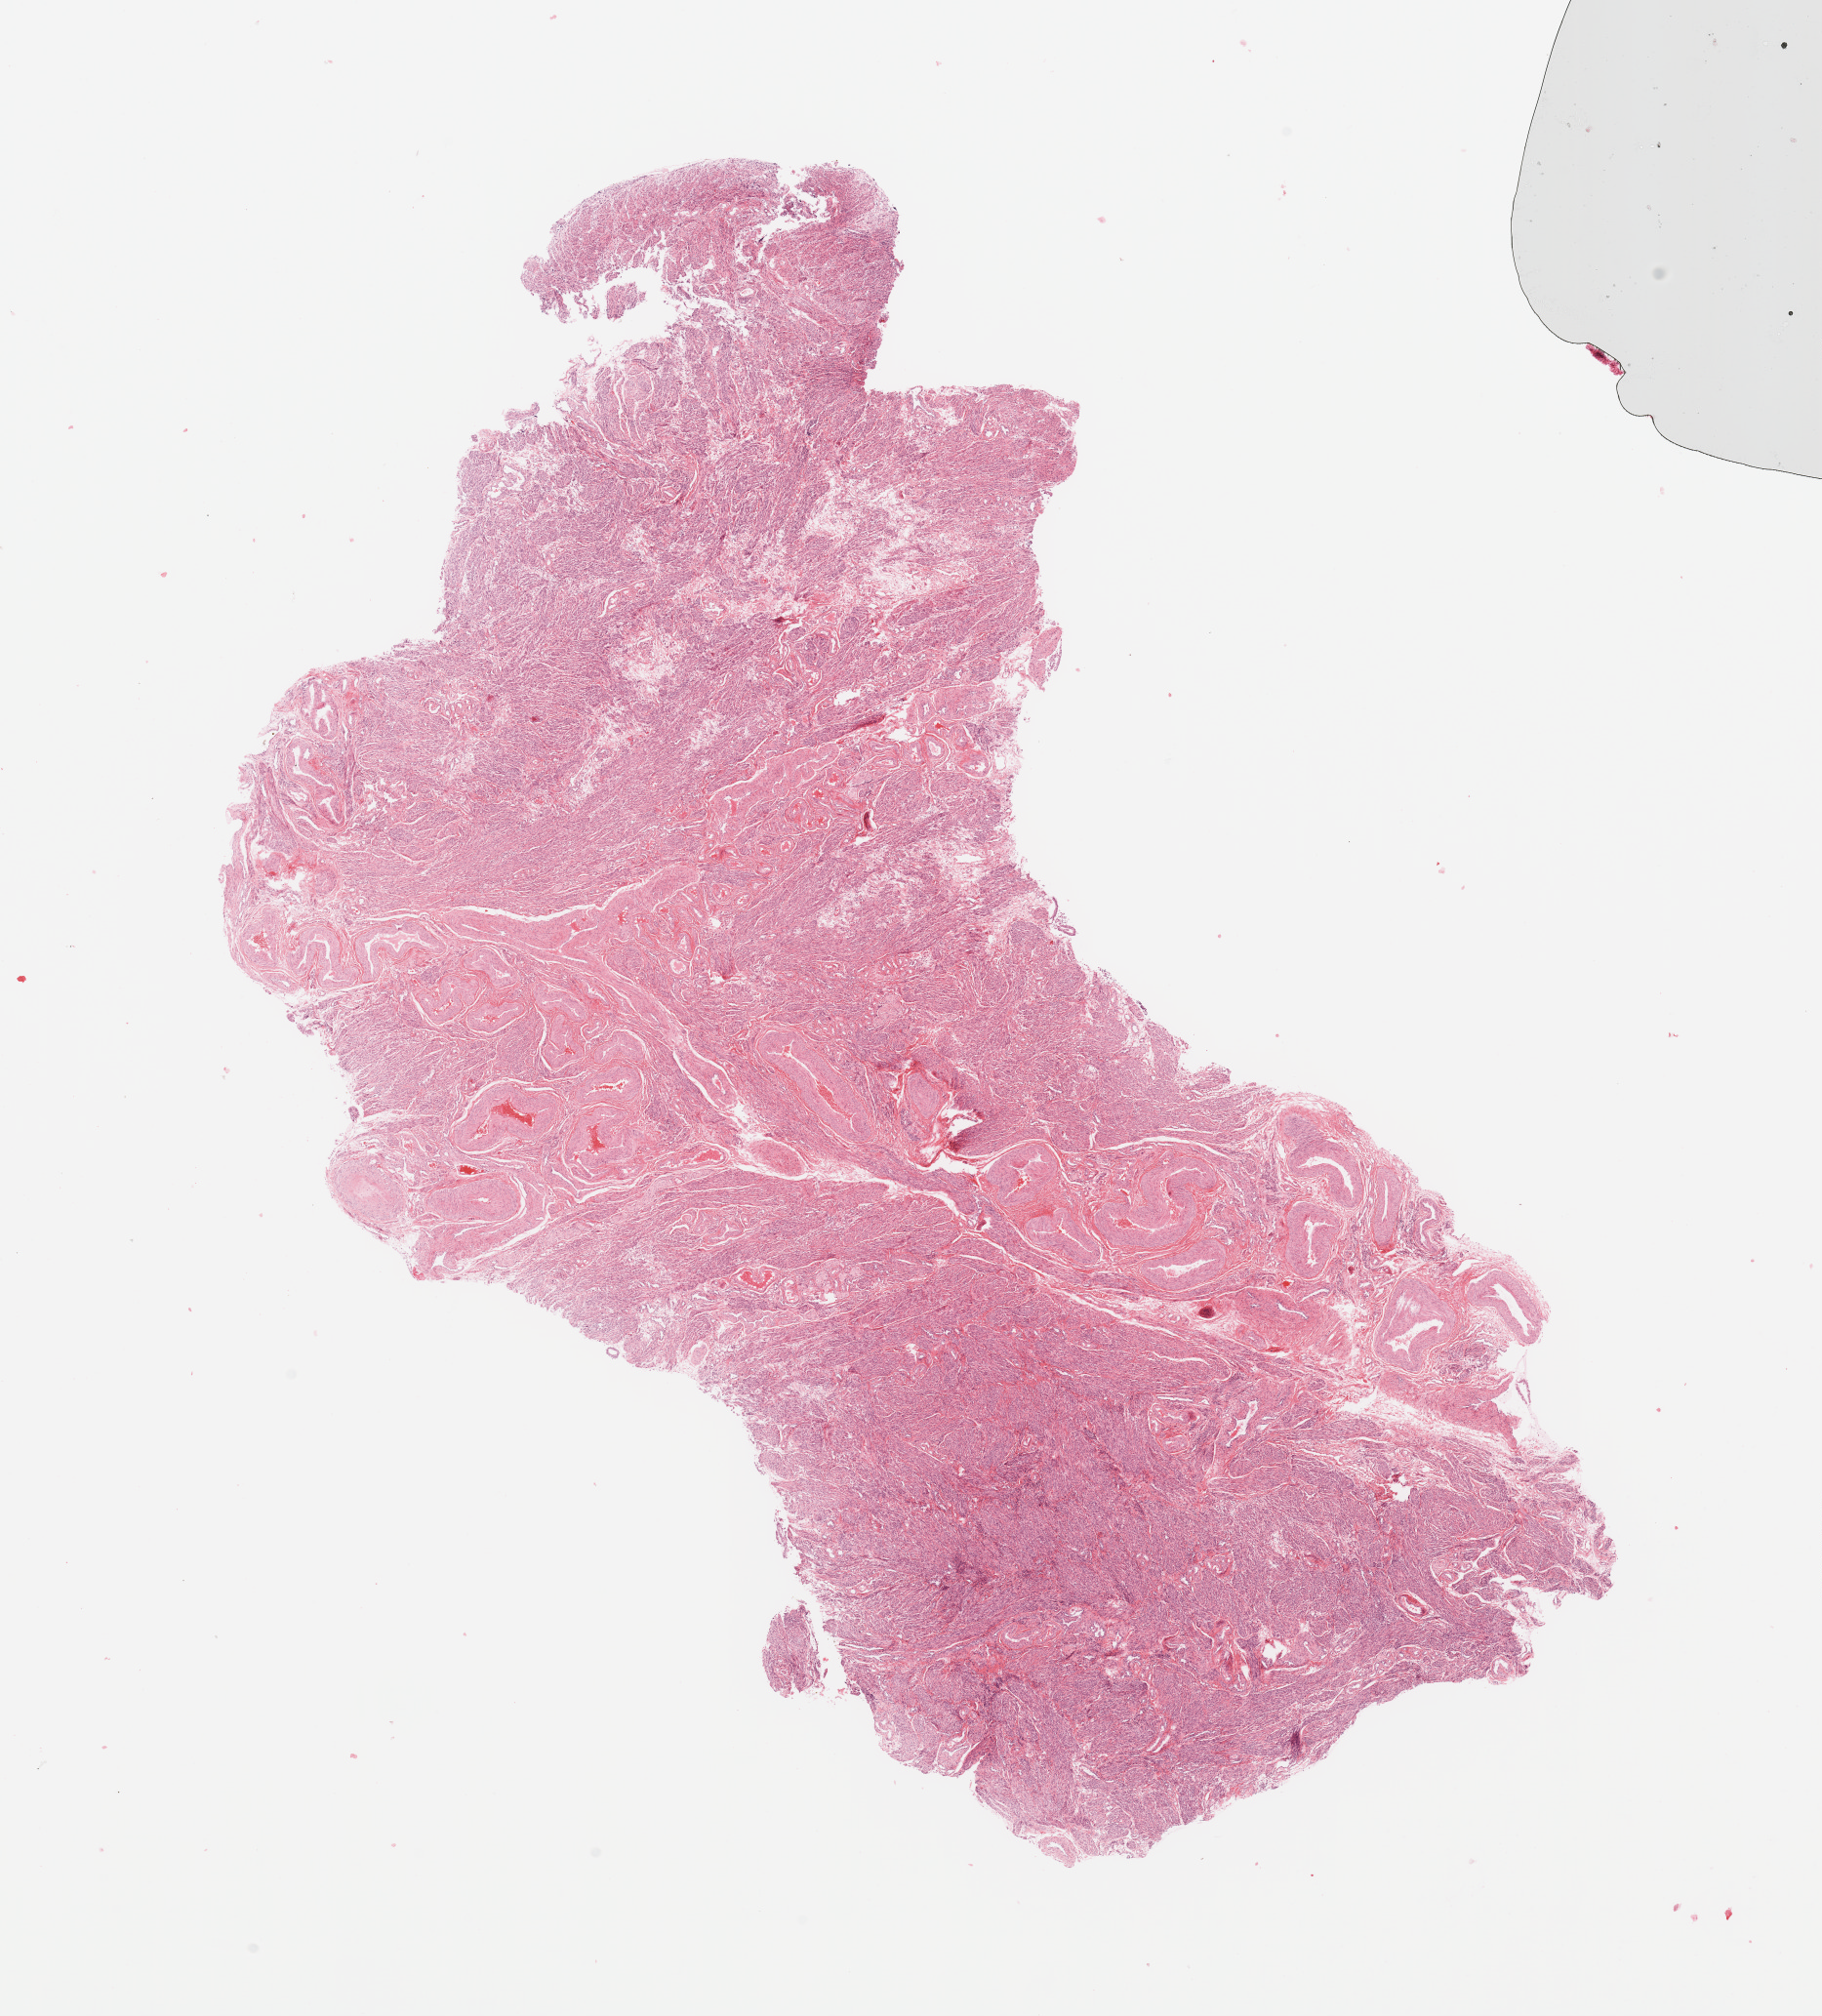
Hematoxylin and eosin (H&E) stained whole-slide image — a low-resolution overview of the entire scanned area, about 14.8 x 16.3 mm (acquisition: 20x scan). Uterus, normal (non-tumour) tissue. Patient: female, age 57 years.
• this section: normal (non-tumour) tissue from the same patient
• patient diagnosis: Endometrioid adenocarcinoma, NOS